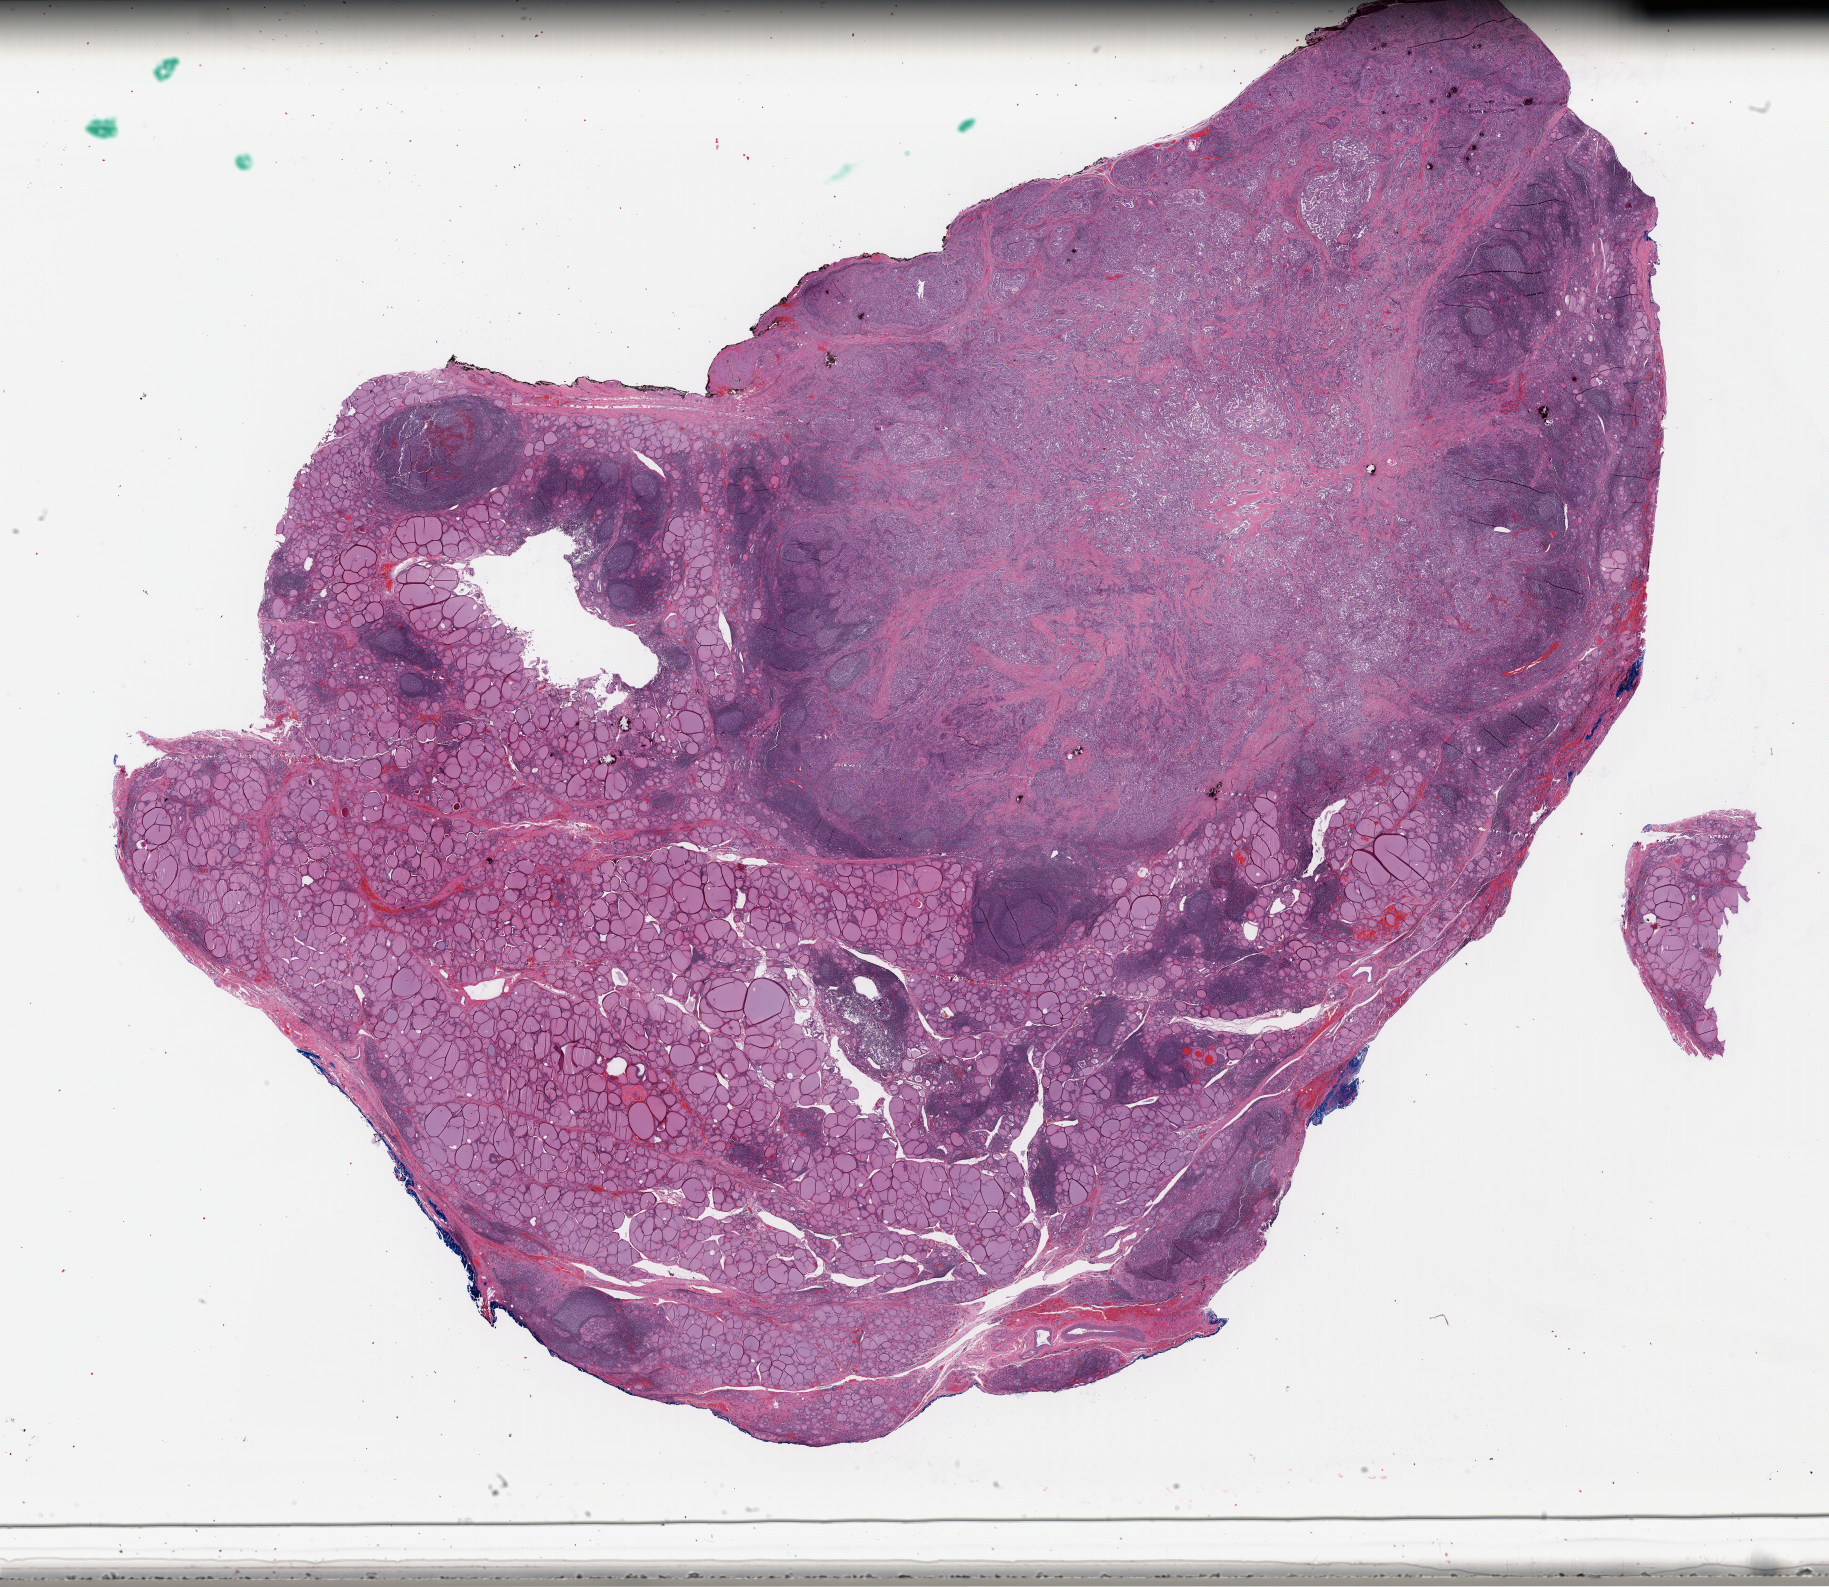
Whole-slide histology image, Hematoxylin and eosin (H&E) stained — a low-resolution overview of the entire scanned area, about 28.8 x 25.0 mm (from a 40x scan), formalin-fixed paraffin-embedded (FFPE) diagnostic section, sample: primary tumour, thyroid. Patient: female, age at initial diagnosis 44 years.
AJCC pathologic stage: I (7th edition). Pathologic diagnosis: Papillary adenocarcinoma, NOS (thyroid gland). Laterality: bilateral.